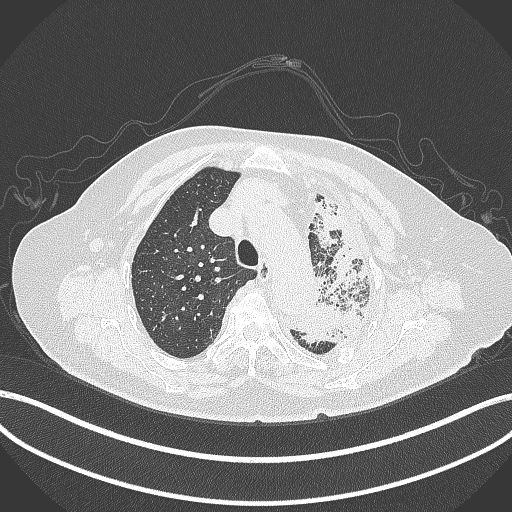
Chest CT, one axial slice. Position 300 of 399 along the scan axis. Reconstruction kernel B70f. Lung window (W 1500 / L -600 HU). 512 × 512 image matrix, field of view 400 × 400 mm. Patient: female, 75 years. Case-level facts recorded for this patient, not image findings: clinical TNM (as recorded): T3 N3 M1.
Structures marked on this image (rectangle marked by the reading radiologist):
- lung tumour (recorded histology: adenocarcinoma): bounding box <292,195,372,356> (left, top, right, bottom; pixels)